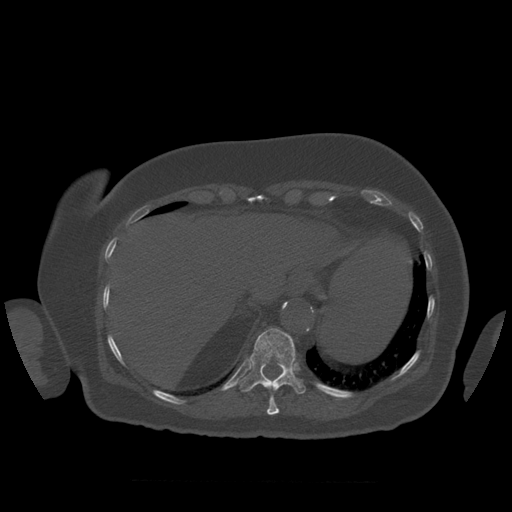
CT including the spine, one axial slice; slice 325 of 399 in the series (ordered by position); reconstruction kernel STANDARD; bone window (W 1800 / L 400 HU); 1.25 mm slice thickness; 512 × 512 image matrix, field of view 404 × 404 mm. Patient age 81 years. Case-level facts recorded for this patient, not image findings: primary cancer: renal; vertebrae with lytic lesions (as recorded): L1.
Annotated regions visible in this slice (semi-automatic segmentation, software-assisted and operator-edited):
- T10 vertebra: bounding box (x1, y1, x2, y2) in pixels: (267, 398, 280, 416)
- T11 vertebra: (238, 328, 306, 395)